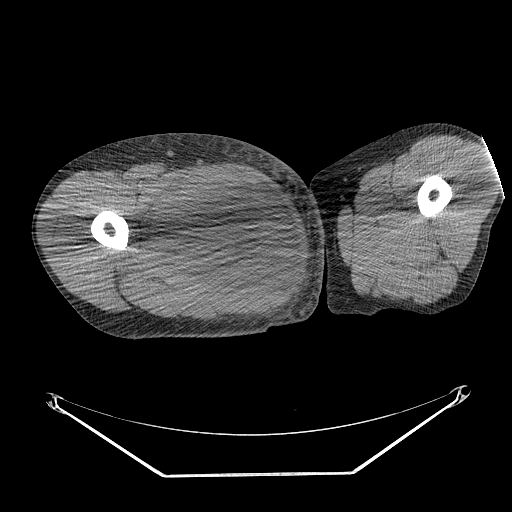
CT of an extremity soft-tissue mass (from a PET/CT study), one axial slice. Position 254 of 311 along the scan axis. Reconstruction kernel STANDARD. 140 kVp. Soft-tissue window (W 400 / L 40 HU). 512 × 512 image matrix, field of view 500 × 500 mm. Male patient. From the clinical record (not read from this slice): histological type: undifferentiated - pleiomorphic; grade: high; site of the primary tumour: right thigh.
Structures marked on this image (expert contour drawn on MRI and transferred to this co-registered scan by the dataset authors):
- gross tumour volume including surrounding oedema: bounding box (x1, y1, x2, y2) in pixels: (137, 171, 263, 271)
- gross tumour volume (mass): (153, 173, 261, 268)